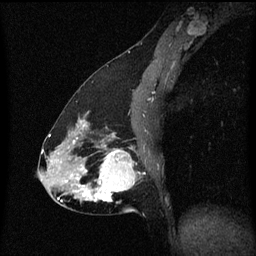
Breast MRI (dynamic contrast-enhanced), one sagittal slice. Position 29 of 60 along the scan axis. Dynamic contrast-enhanced series, image 2 of 3 at this slice position (ordered by acquisition). 1.5 T. TE 4.2 ms, TR 8.4 ms. 2 mm slice thickness. 256 × 256 image matrix. Female patient, age 47 years.
Annotated regions visible in this slice (semi-automatically segmented with operator editing):
- analysis volume of interest (the breast-tissue region the enhancement analysis was run in; not a lesion): bounding box (x1, y1, x2, y2) in pixels: (81, 138, 146, 213)
- tumour enhancement mask (voxels above the 70 % enhancement threshold inside the analysis volume of interest): (81, 146, 136, 203)